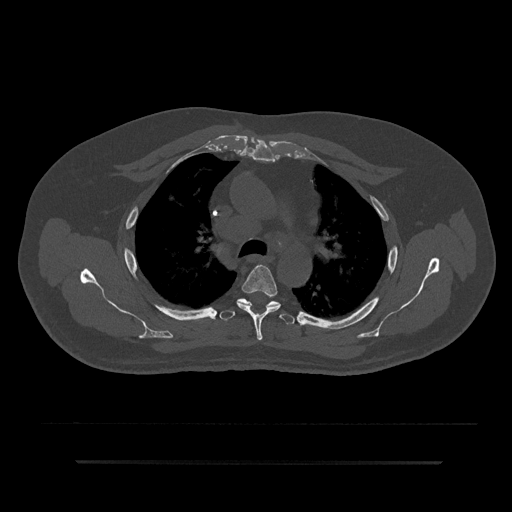
CT including the spine, one axial slice. Position 605 of 797 along the scan axis. Reconstruction kernel Br40s/3. Bone window (W 1800 / L 400 HU). 0.5 mm slice thickness. 512 × 512 image matrix, field of view 464 × 464 mm. Male patient, age 59 years. From the clinical record (not read from this slice): primary cancer: bile ducts.
Outlined on this slice (semi-automatic segmentation, software-assisted and operator-edited):
- T4 vertebra: bounding box <237,265,281,341> (left, top, right, bottom; pixels)
- T5 vertebra: <219,298,298,325>